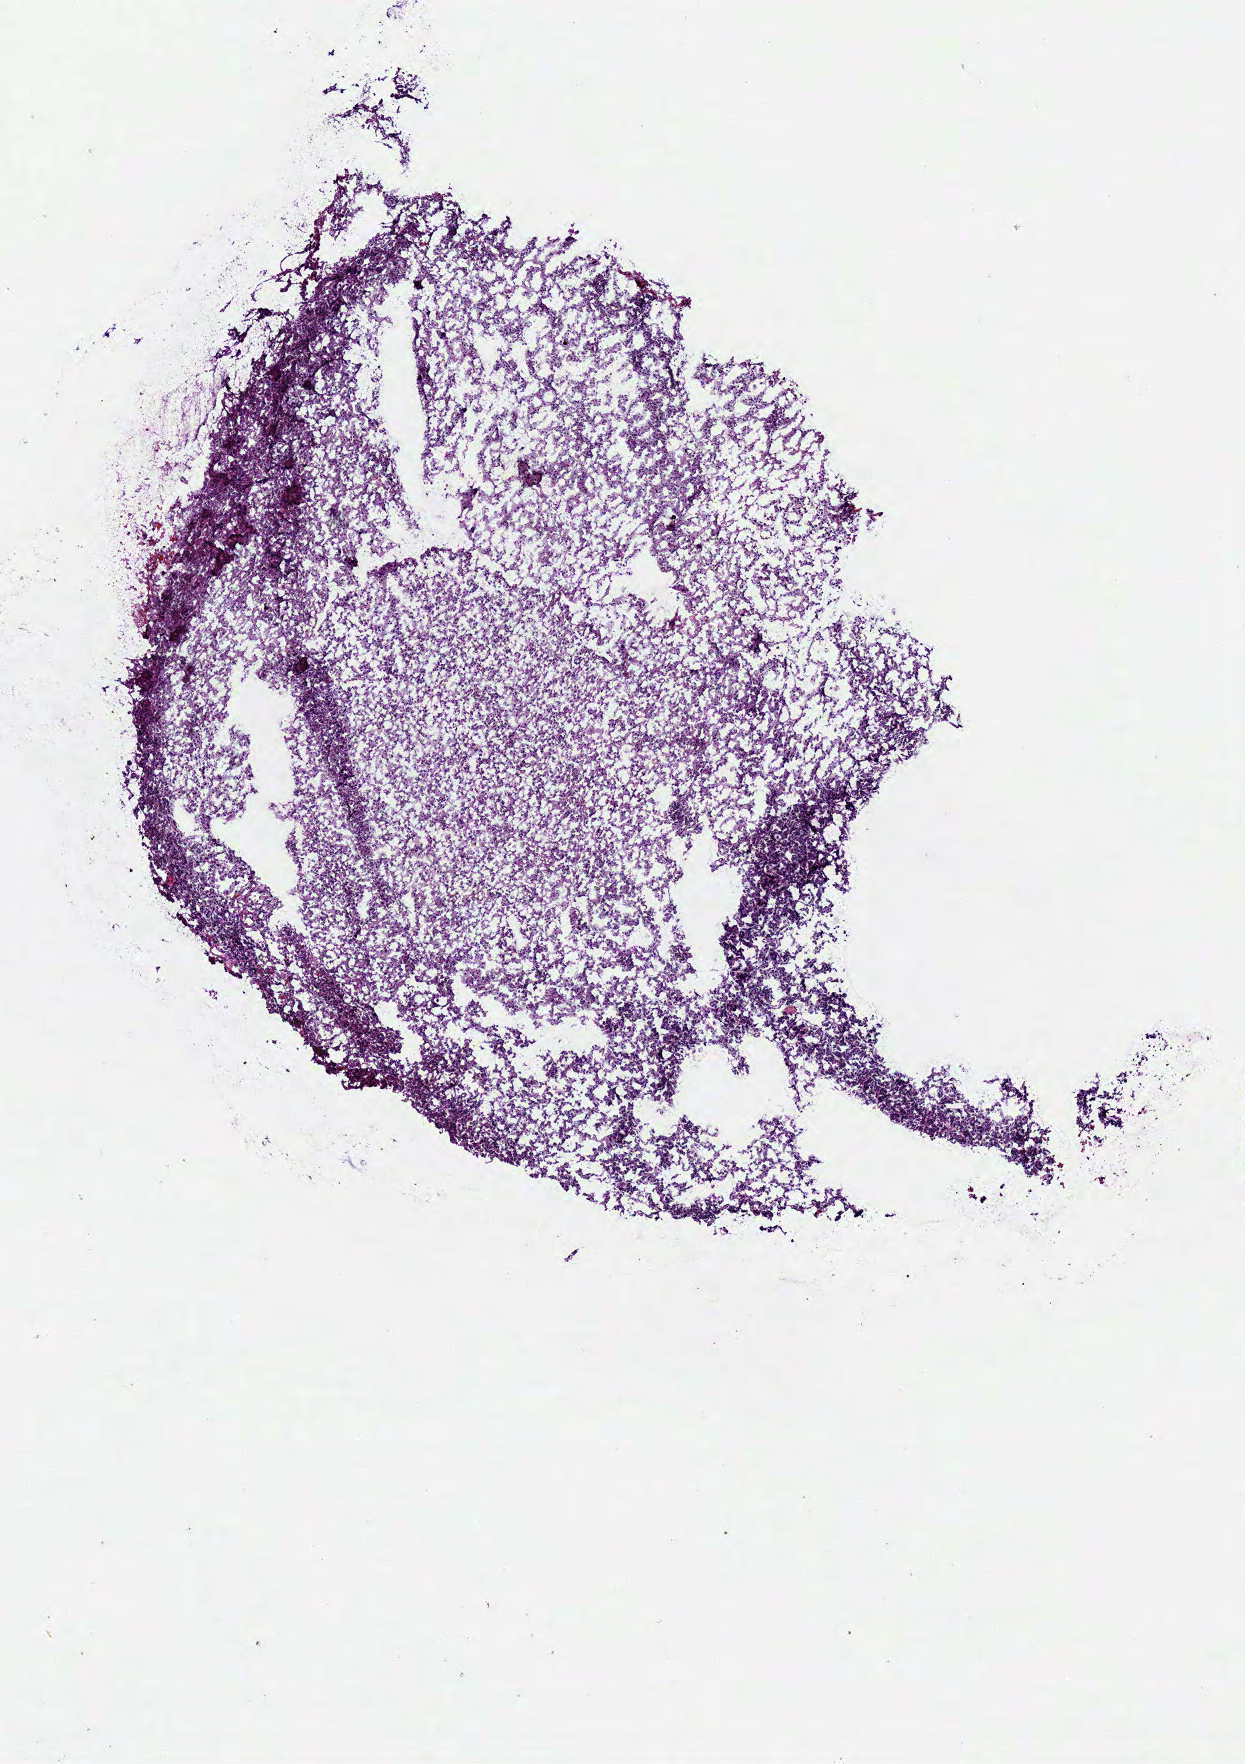
Hematoxylin and eosin (H&E) stained whole-slide image — whole scanned area (about 4.9 x 6.9 mm, from a 40x scan) shown as a low-resolution overview, frozen section from the bottom of the tissue portion, brain, primary tumour sample. Female, age 66 years at initial diagnosis.
Histologic diagnosis: Oligodendroglioma, NOS.